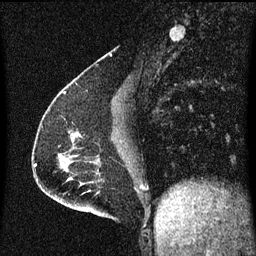
Breast MRI (dynamic contrast-enhanced), one sagittal slice. Position 22 of 60 along the scan axis. Dynamic contrast-enhanced series, image 2 of 3 at this slice position (ordered by acquisition). 1.5 T. TE 4.2 ms, TR 8 ms. 256 × 256 image matrix. Patient: female, 51 years.
Outlined on this slice (semi-automatic segmentation, software-assisted and operator-edited):
- analysis volume of interest (the breast-tissue region the enhancement analysis was run in; not a lesion): bounding box <70,132,83,149> (left, top, right, bottom; pixels)
- tumour enhancement mask (voxels above the 70 % enhancement threshold inside the analysis volume of interest): <74,132,79,143>